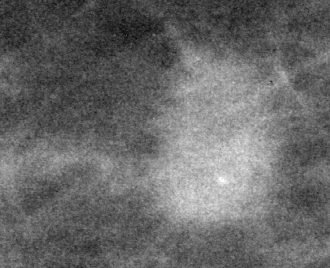
Region of interest cut from a scanned film mammogram (one marked finding); right breast; MLO view; BI-RADS breast density category 1 (scale 1–4).
- Mass, shape oval, margins spiculated; BI-RADS assessment category 5; pathology result (as recorded, not read from the image): malignant.